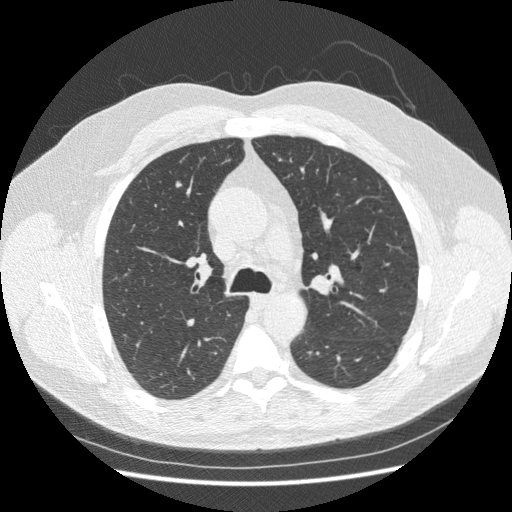
Low-dose screening chest CT, one axial slice. Slice 160 of 250 in the series (ordered by position). Reconstruction kernel STANDARD. 120 kVp. Lung window (W 1500 / L -600 HU). 1.25 mm slice thickness. 512 × 512 image matrix, field of view 360 × 360 mm.
Structures marked on this image (manually delineated by an expert):
- lesion 1 (tumor, upper lobe of right lung): bounding box <175,179,183,189> (left, top, right, bottom; pixels)